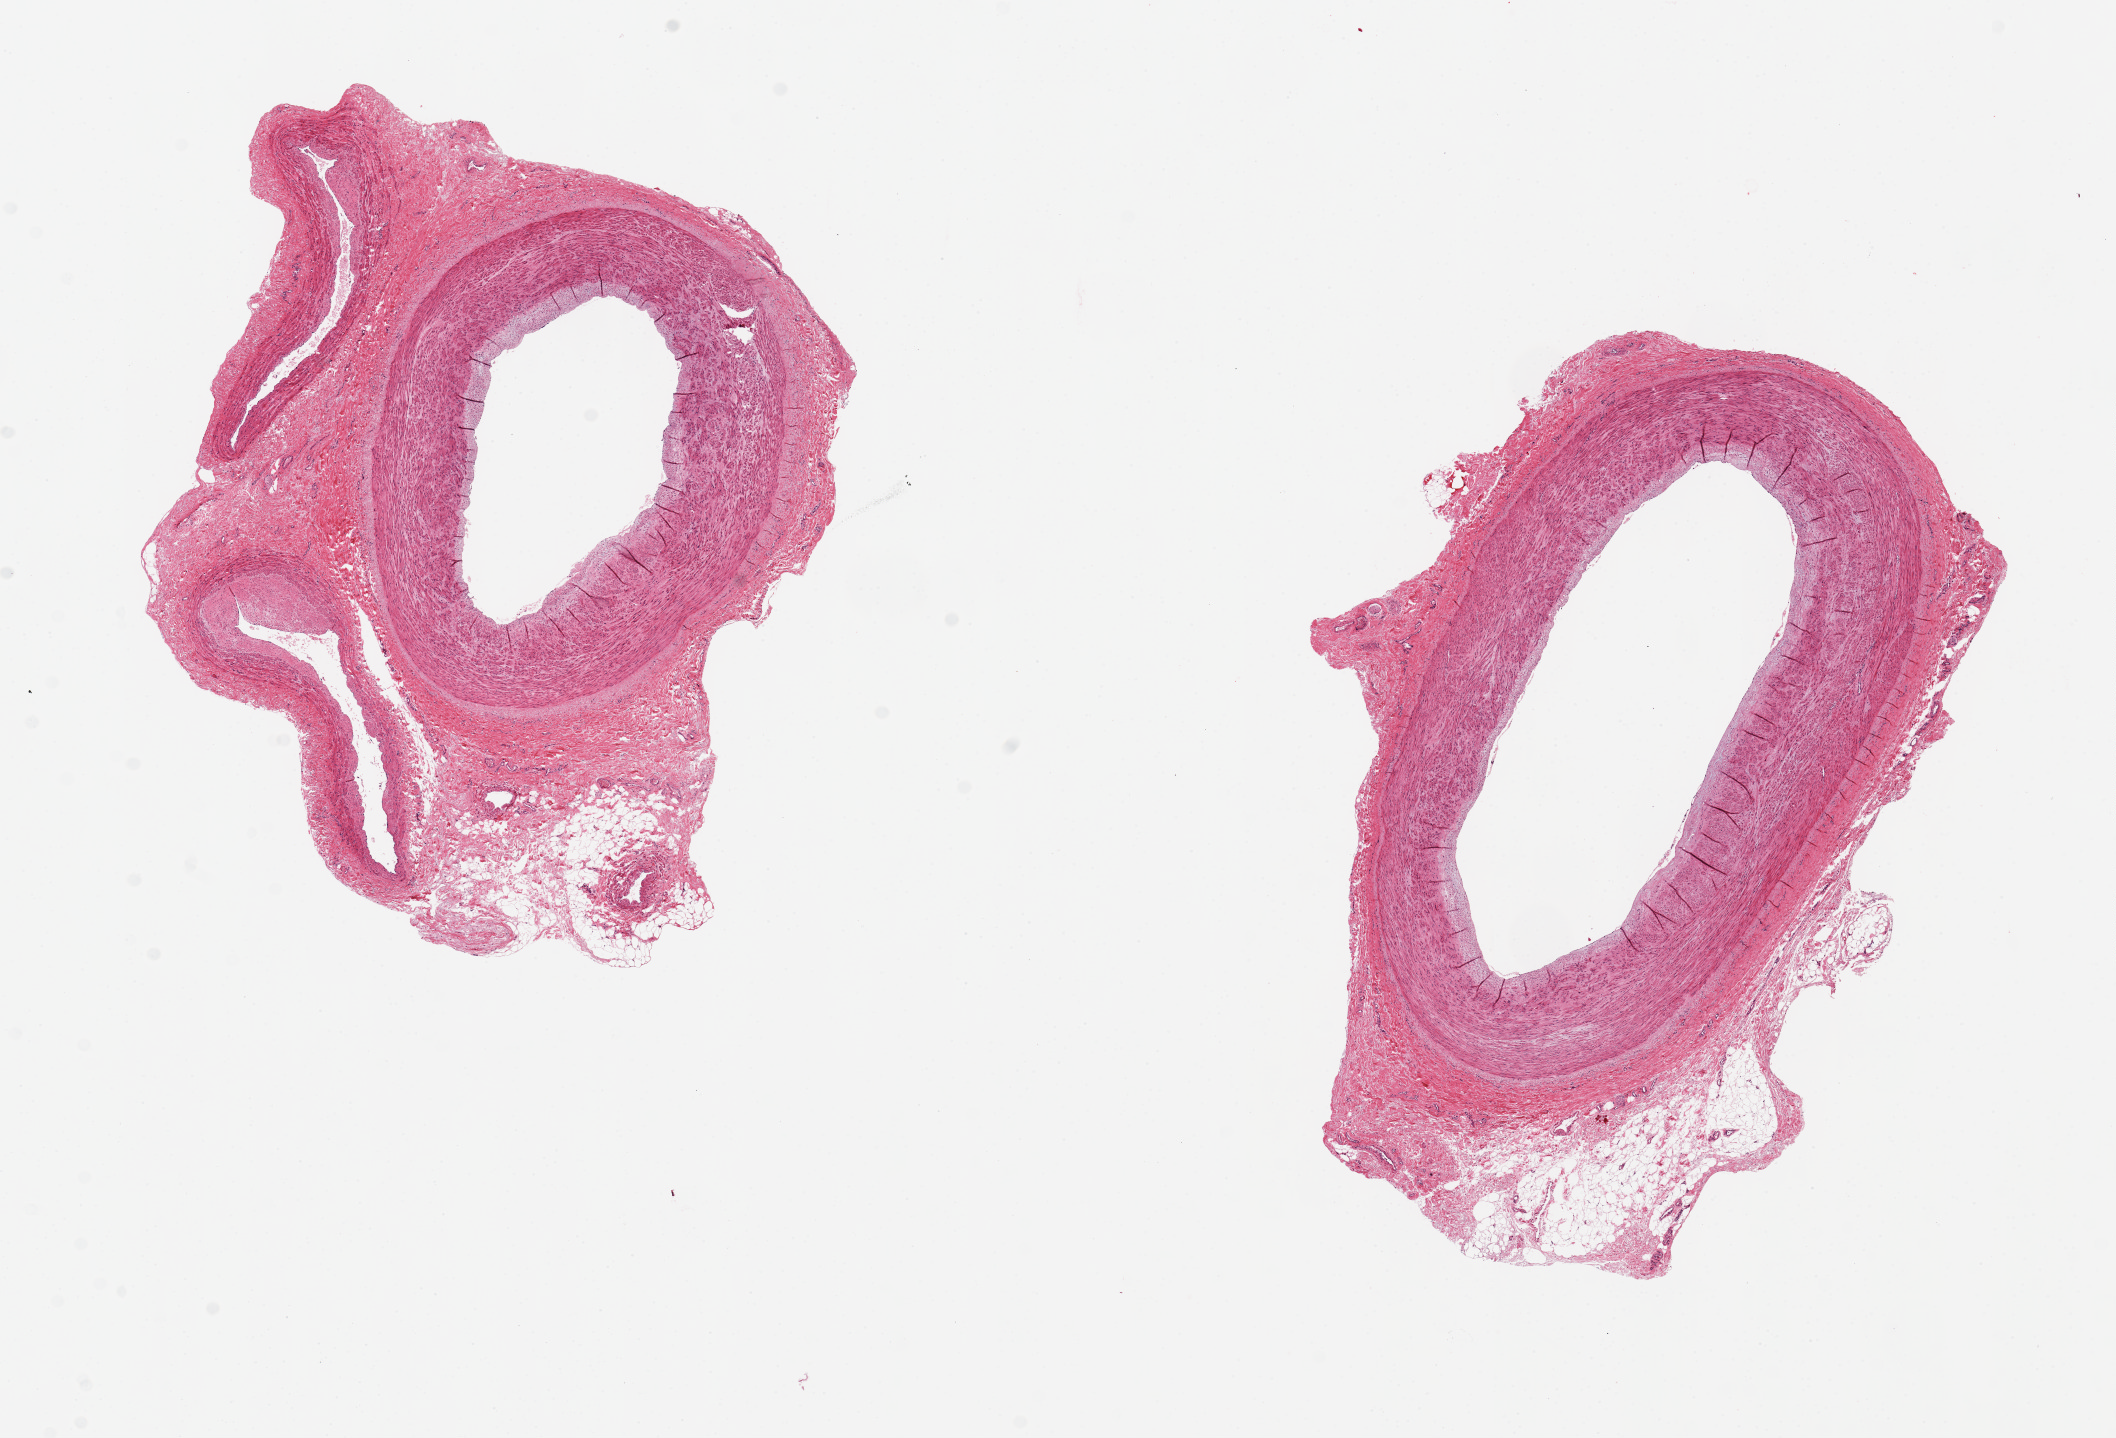
Digitized hematoxylin and eosin (H&E)-stained section — shown as a low-resolution overview of the whole scanned area (about 16.7 x 11.4 mm), PAXgene-fixed, paraffin-embedded tissue, sampled site (target tissue): tibial artery, donor tissue sample. Donor: male.
- pathologist's review note for this sample: 2 arteries ~4 mm and 2 veins; minimal intimal thickening